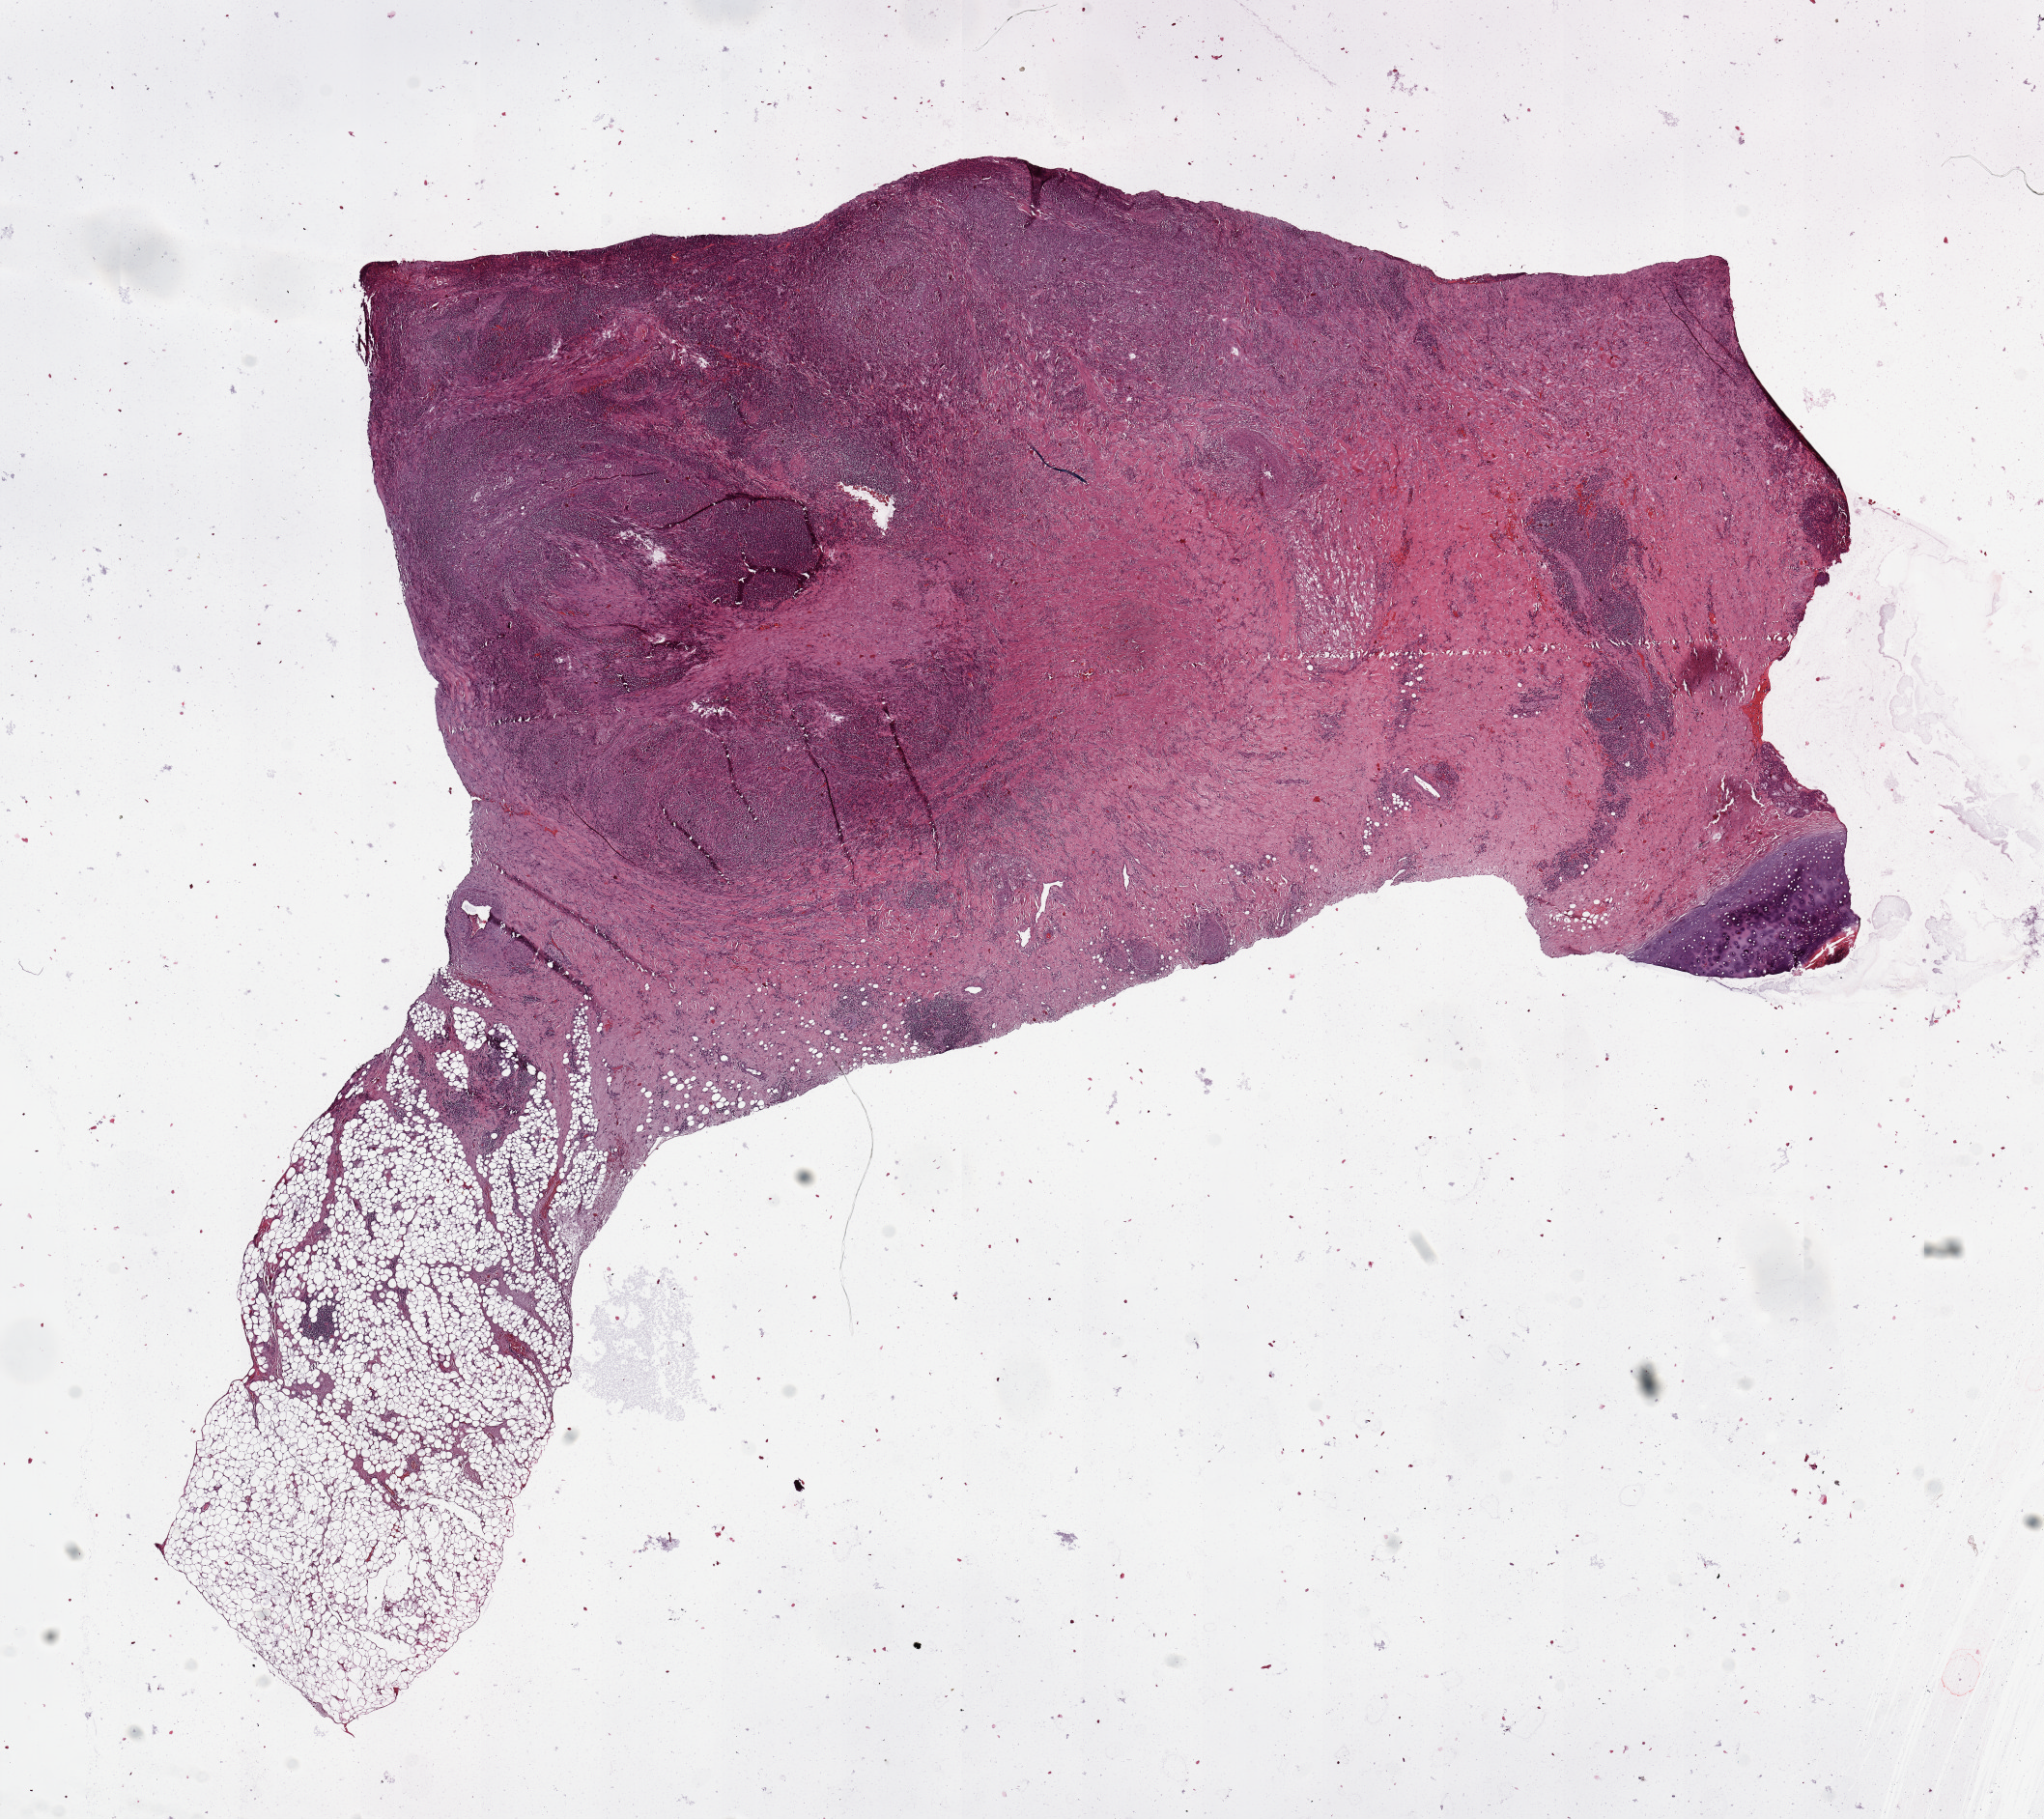
Digitized Hematoxylin and eosin (H&E) stained tissue section (whole slide) — whole scanned area (about 16.7 x 14.9 mm) shown as a low-resolution overview. Lung, tumour tissue. 58-year-old male patient. Histologic grade: G2 (moderately differentiated).
Histologic diagnosis: Squamous cell carcinoma, NOS. AJCC pathologic stage: IIB. Primary tumour site (as recorded): left upper lobe.